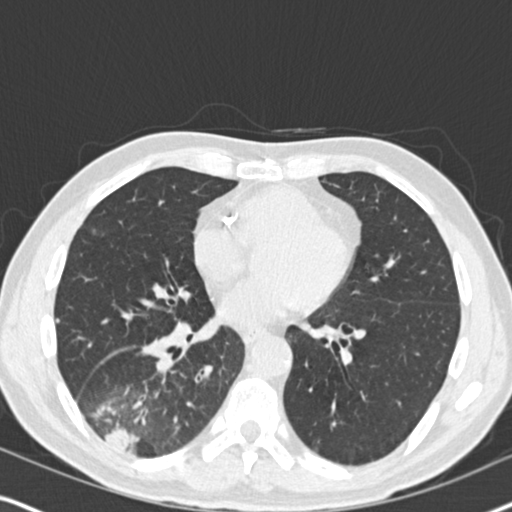
Axial slice from a low-dose chest CT screening exam. Second screening round (one year after baseline). Lung window (W 1500 / L -600 HU). 512 × 512 image matrix. Male participant, aged 61 years at enrolment.
- Expert reader's lesion annotation, bounding box (x1, y1, x2, y2) in pixels: (65, 348, 194, 468).
- Reader record for this screening exam (exam-level; its link to the box is not recorded): non-calcified nodule or mass ≥4 mm, right lower lobe, 90 × 80 mm, soft tissue attenuation, pre-existing on the prior screen: yes; interval growth: yes.
- Later outcome: lung cancer diagnosed 20 days after this screen — bronchiolo-alveolar adenocarcinoma, NOS, right lower lobe, moderately differentiated (G2), stage IIIB (AJCC 6th edition), 90 mm at pathology.